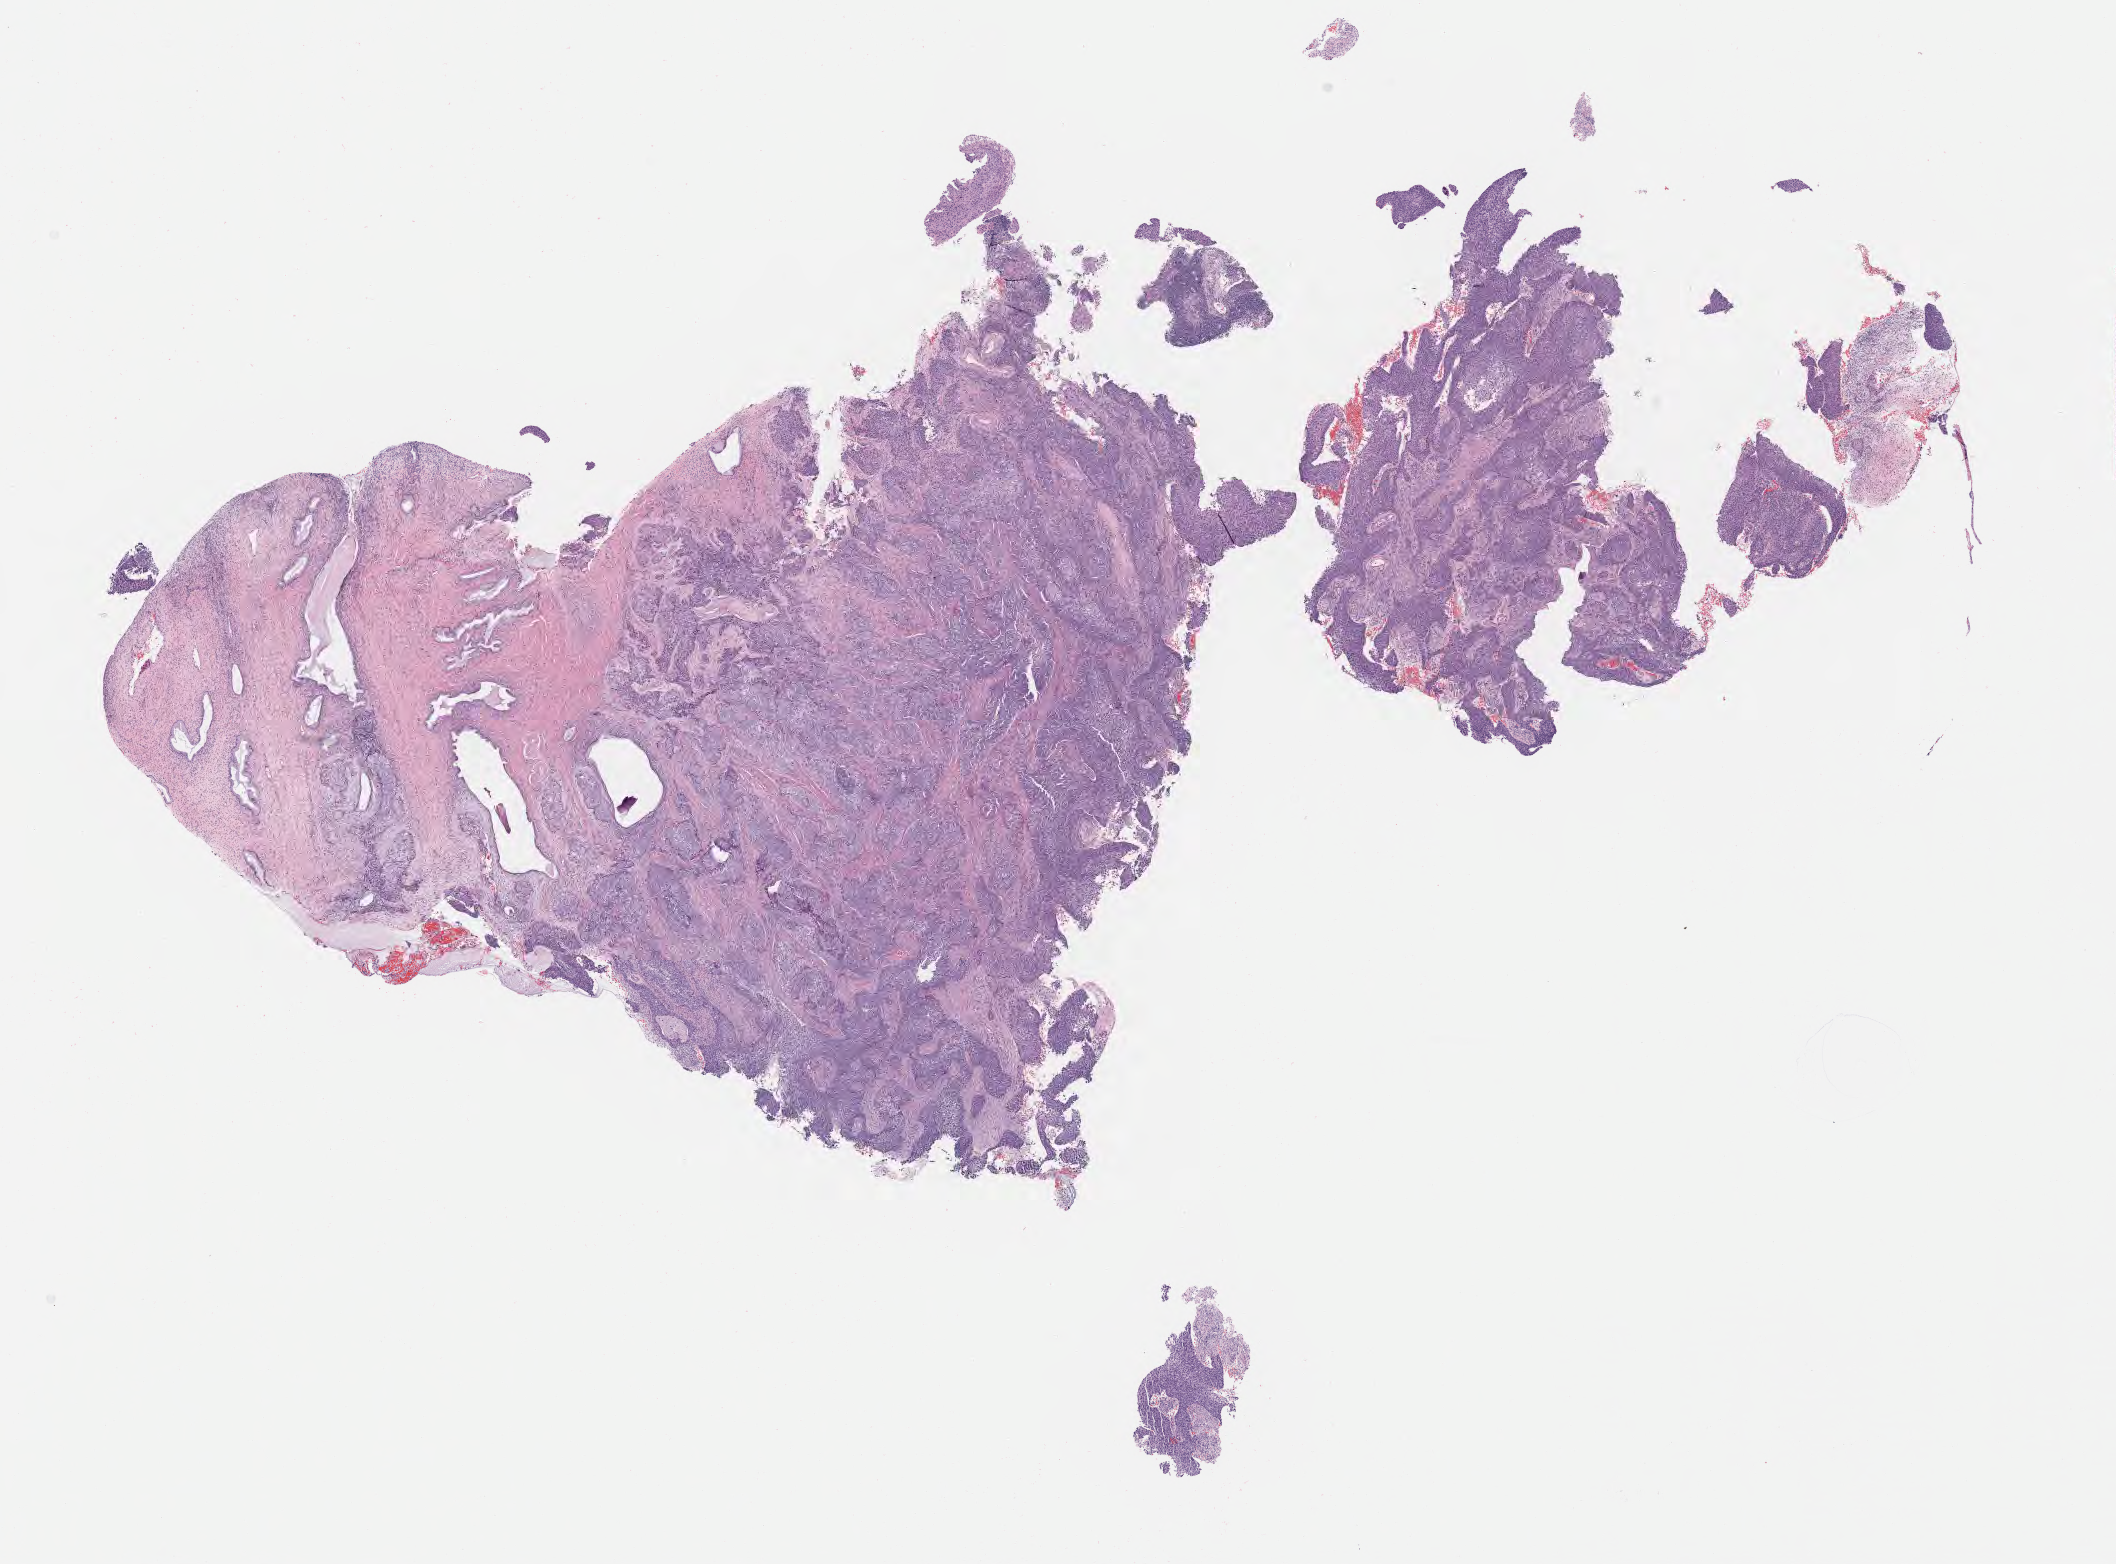
Digitized hematoxylin and eosin (H&E)-stained section, low-resolution overview of the scanned area, about 17.1 x 12.6 mm, specimen: tumor tissue, anatomic site: cervix. Female patient, age 50 years.
Diagnosis: Squamous cell carcinoma, large cell, nonkeratinizing, NOS.